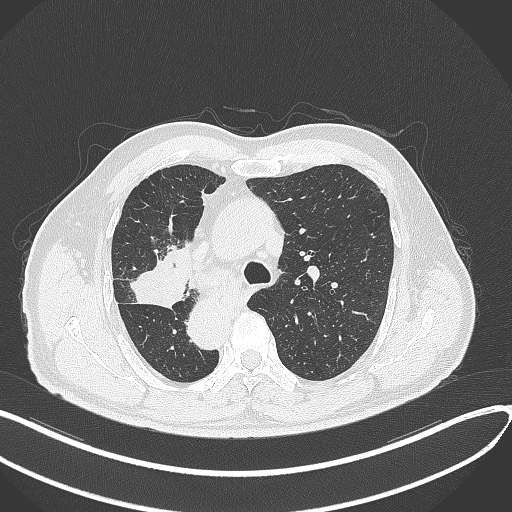
Chest CT, one axial slice; position 214 of 300 along the scan axis; reconstruction kernel B70f; 120 kVp; lung window (W 1500 / L -600 HU); 1 mm slice thickness; 512 × 512 image matrix, field of view 400 × 400 mm. Male patient, age 67 years. Case-level facts recorded for this patient, not image findings: clinical TNM (as recorded): T2a N0 M0.
Outlined on this slice (rectangle marked by the reading radiologist):
- lung tumour (recorded histology: squamous cell carcinoma): bounding box [x1, y1, x2, y2] px = [132, 258, 190, 312]